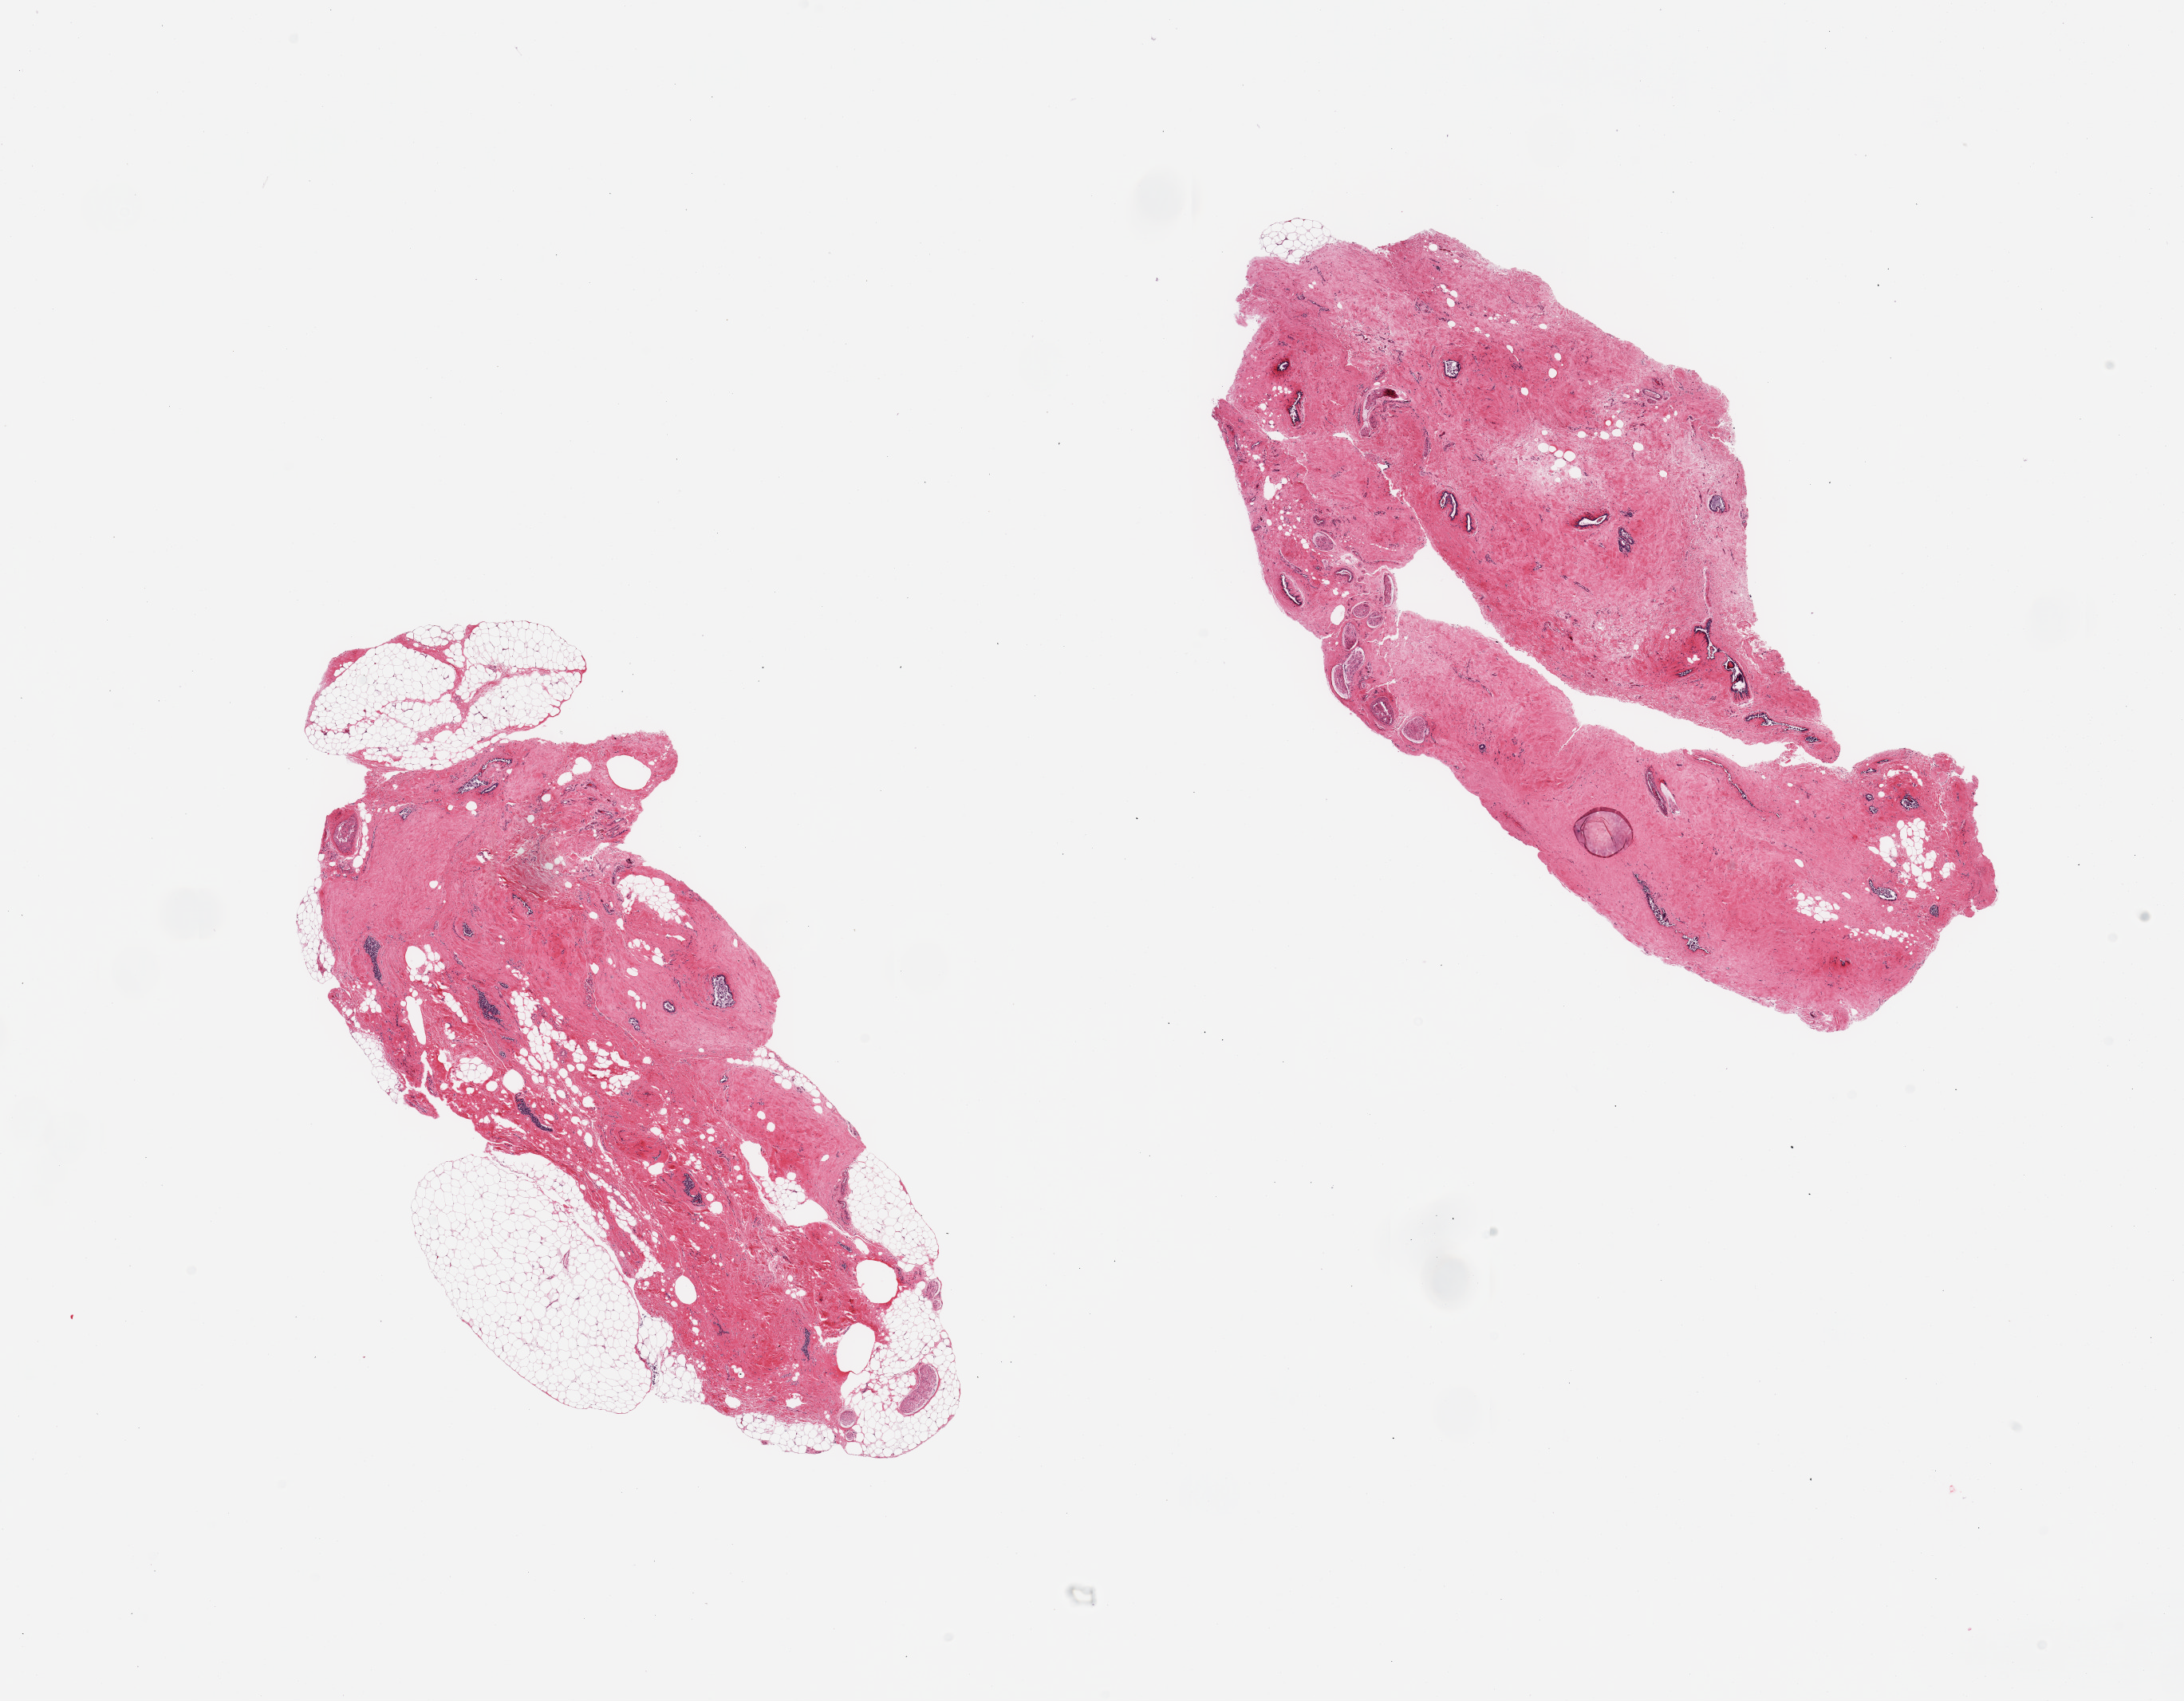
Whole-slide image, H&E stain, brightfield, a low-resolution overview of the entire scanned area, about 21.7 x 16.9 mm, PAXgene-fixed paraffin-embedded (PFPE) section, sampled site (target tissue): breast, tissue donor sample.
Reviewer comment on this tissue sample: 2 pieces; fibroadipose tissue and nerves with gynecomastoid ductal and stromal hyperplasia; sloughed autolyzed ductal epithelium.